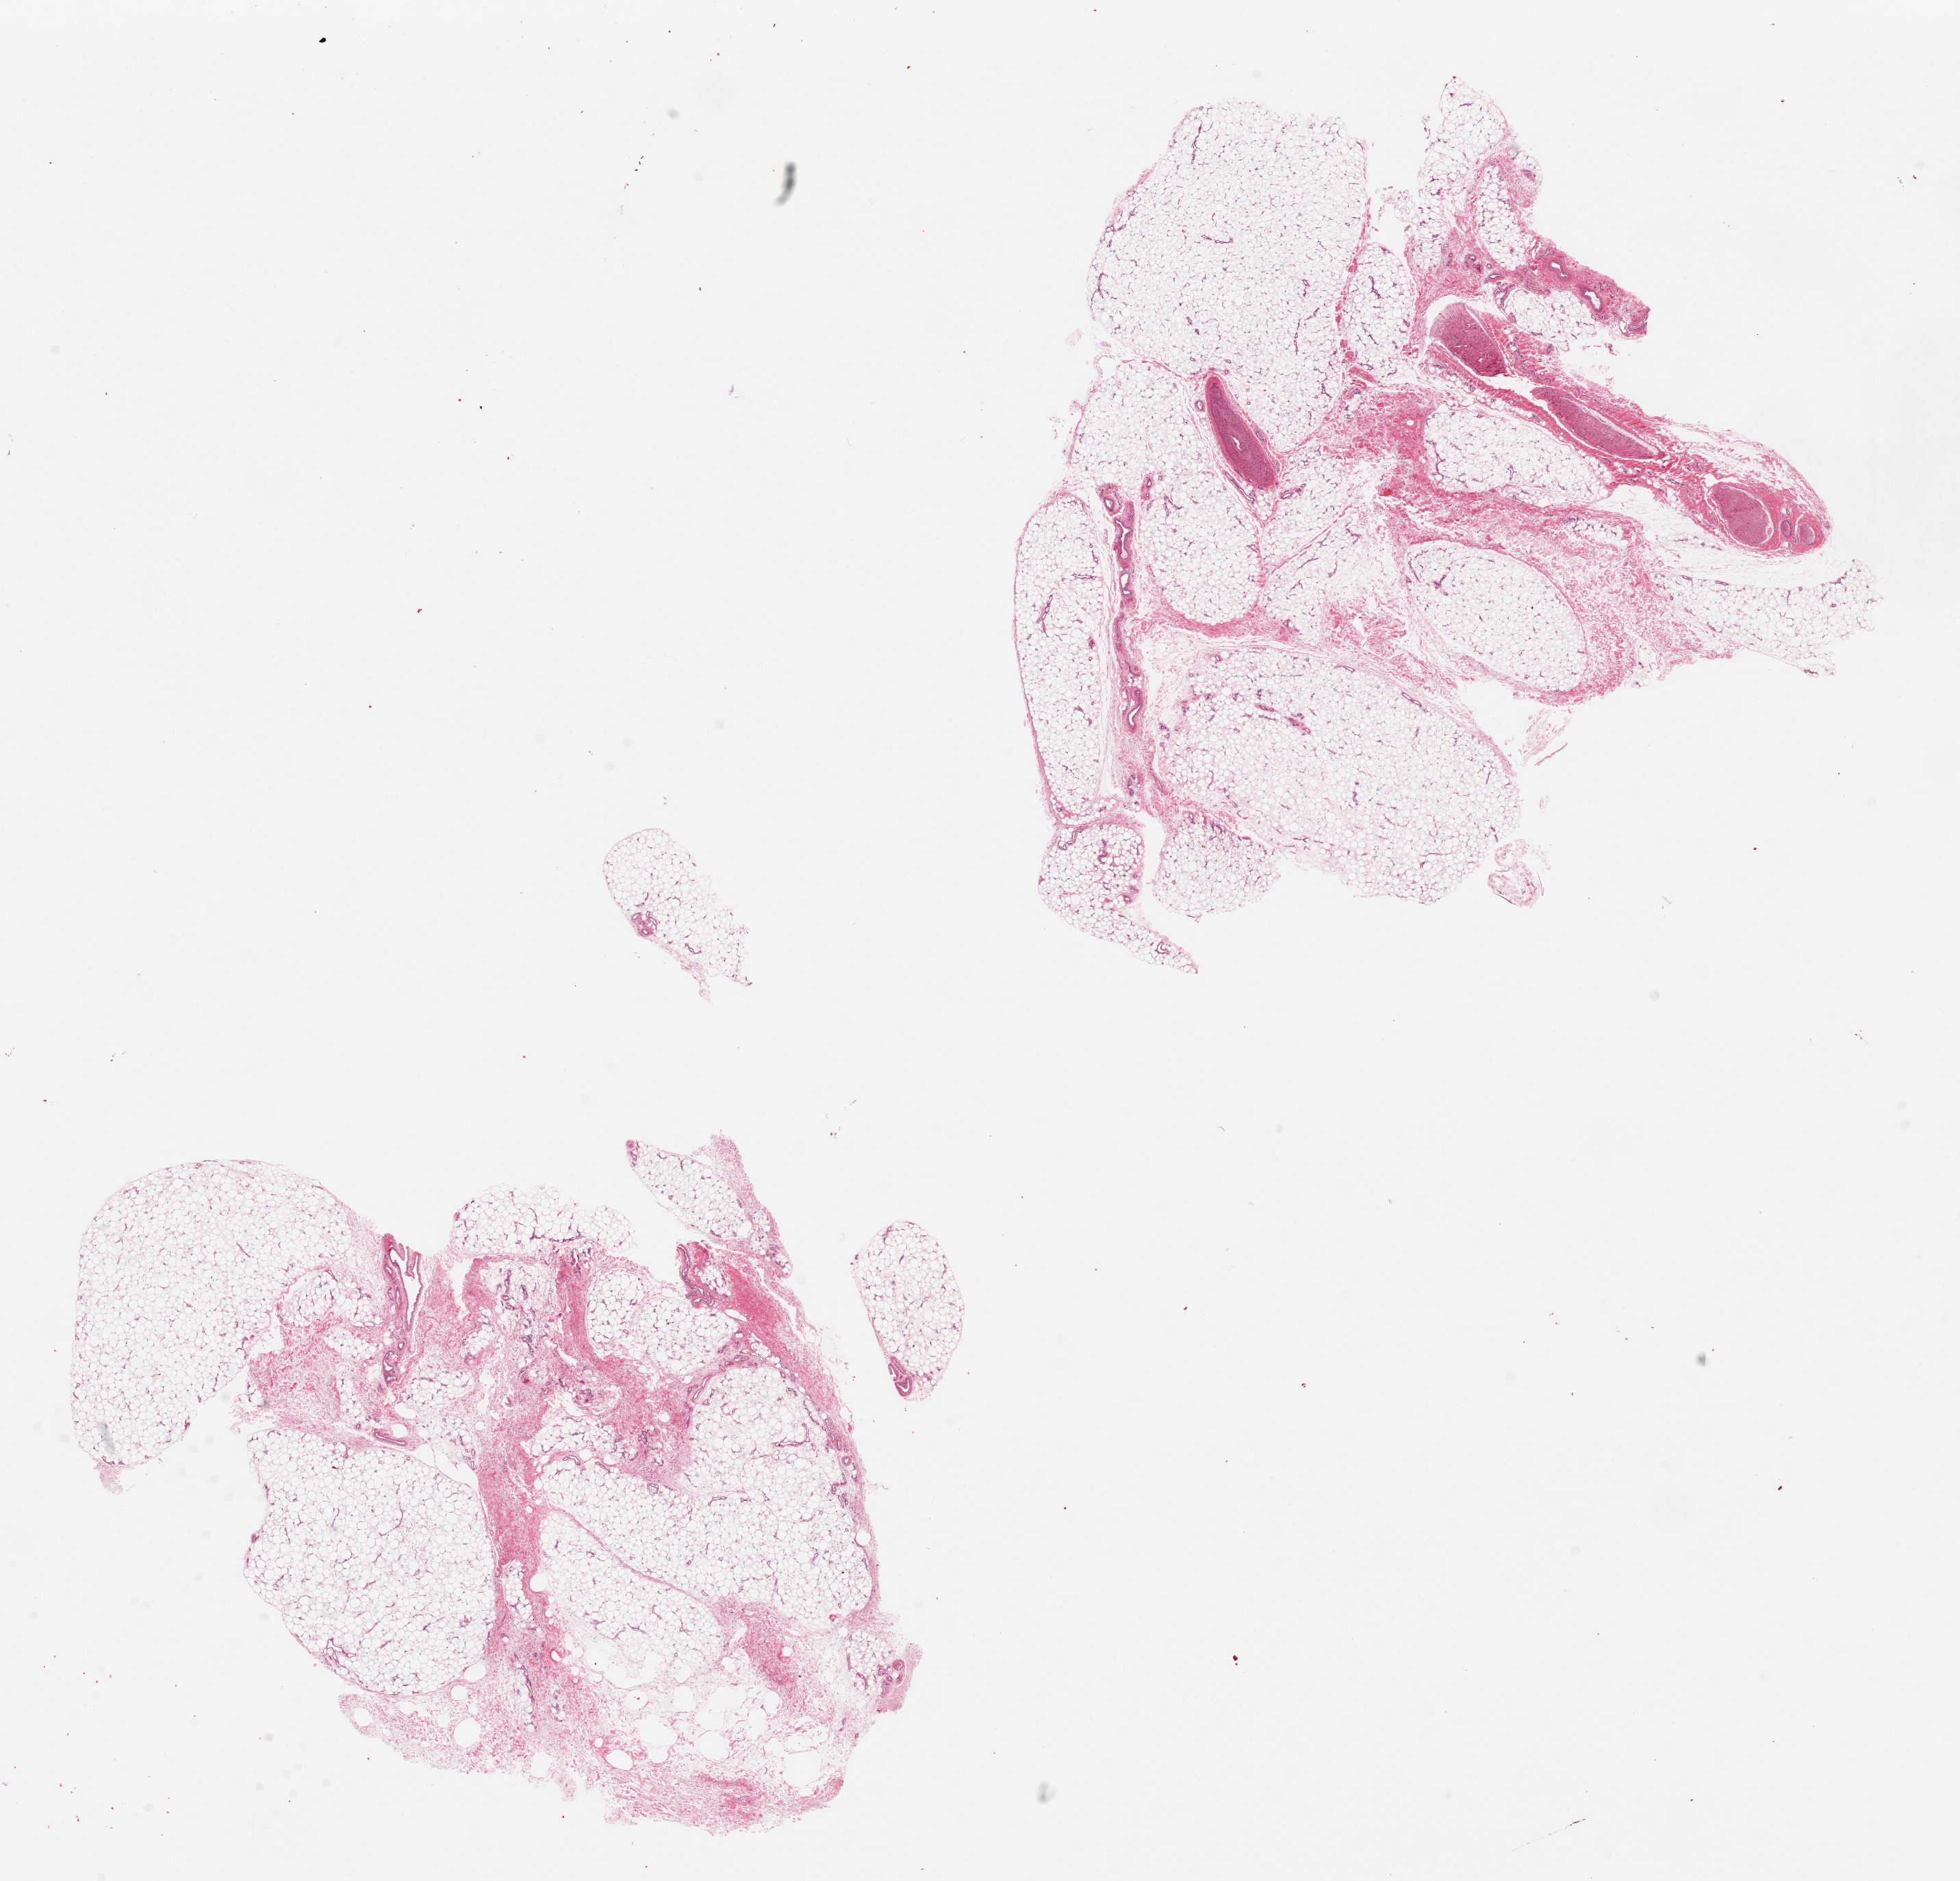
Digitized H&E-stained section — low-resolution overview of the scanned area, about 22.6 x 21.7 mm. PAXgene-fixed paraffin-embedded (PFPE) section. Target tissue: adipose tissue. Tissue donor sample. Donor sex: male.
Reviewer comment on this tissue sample: 2 pieces; 10% fibrovascular component.